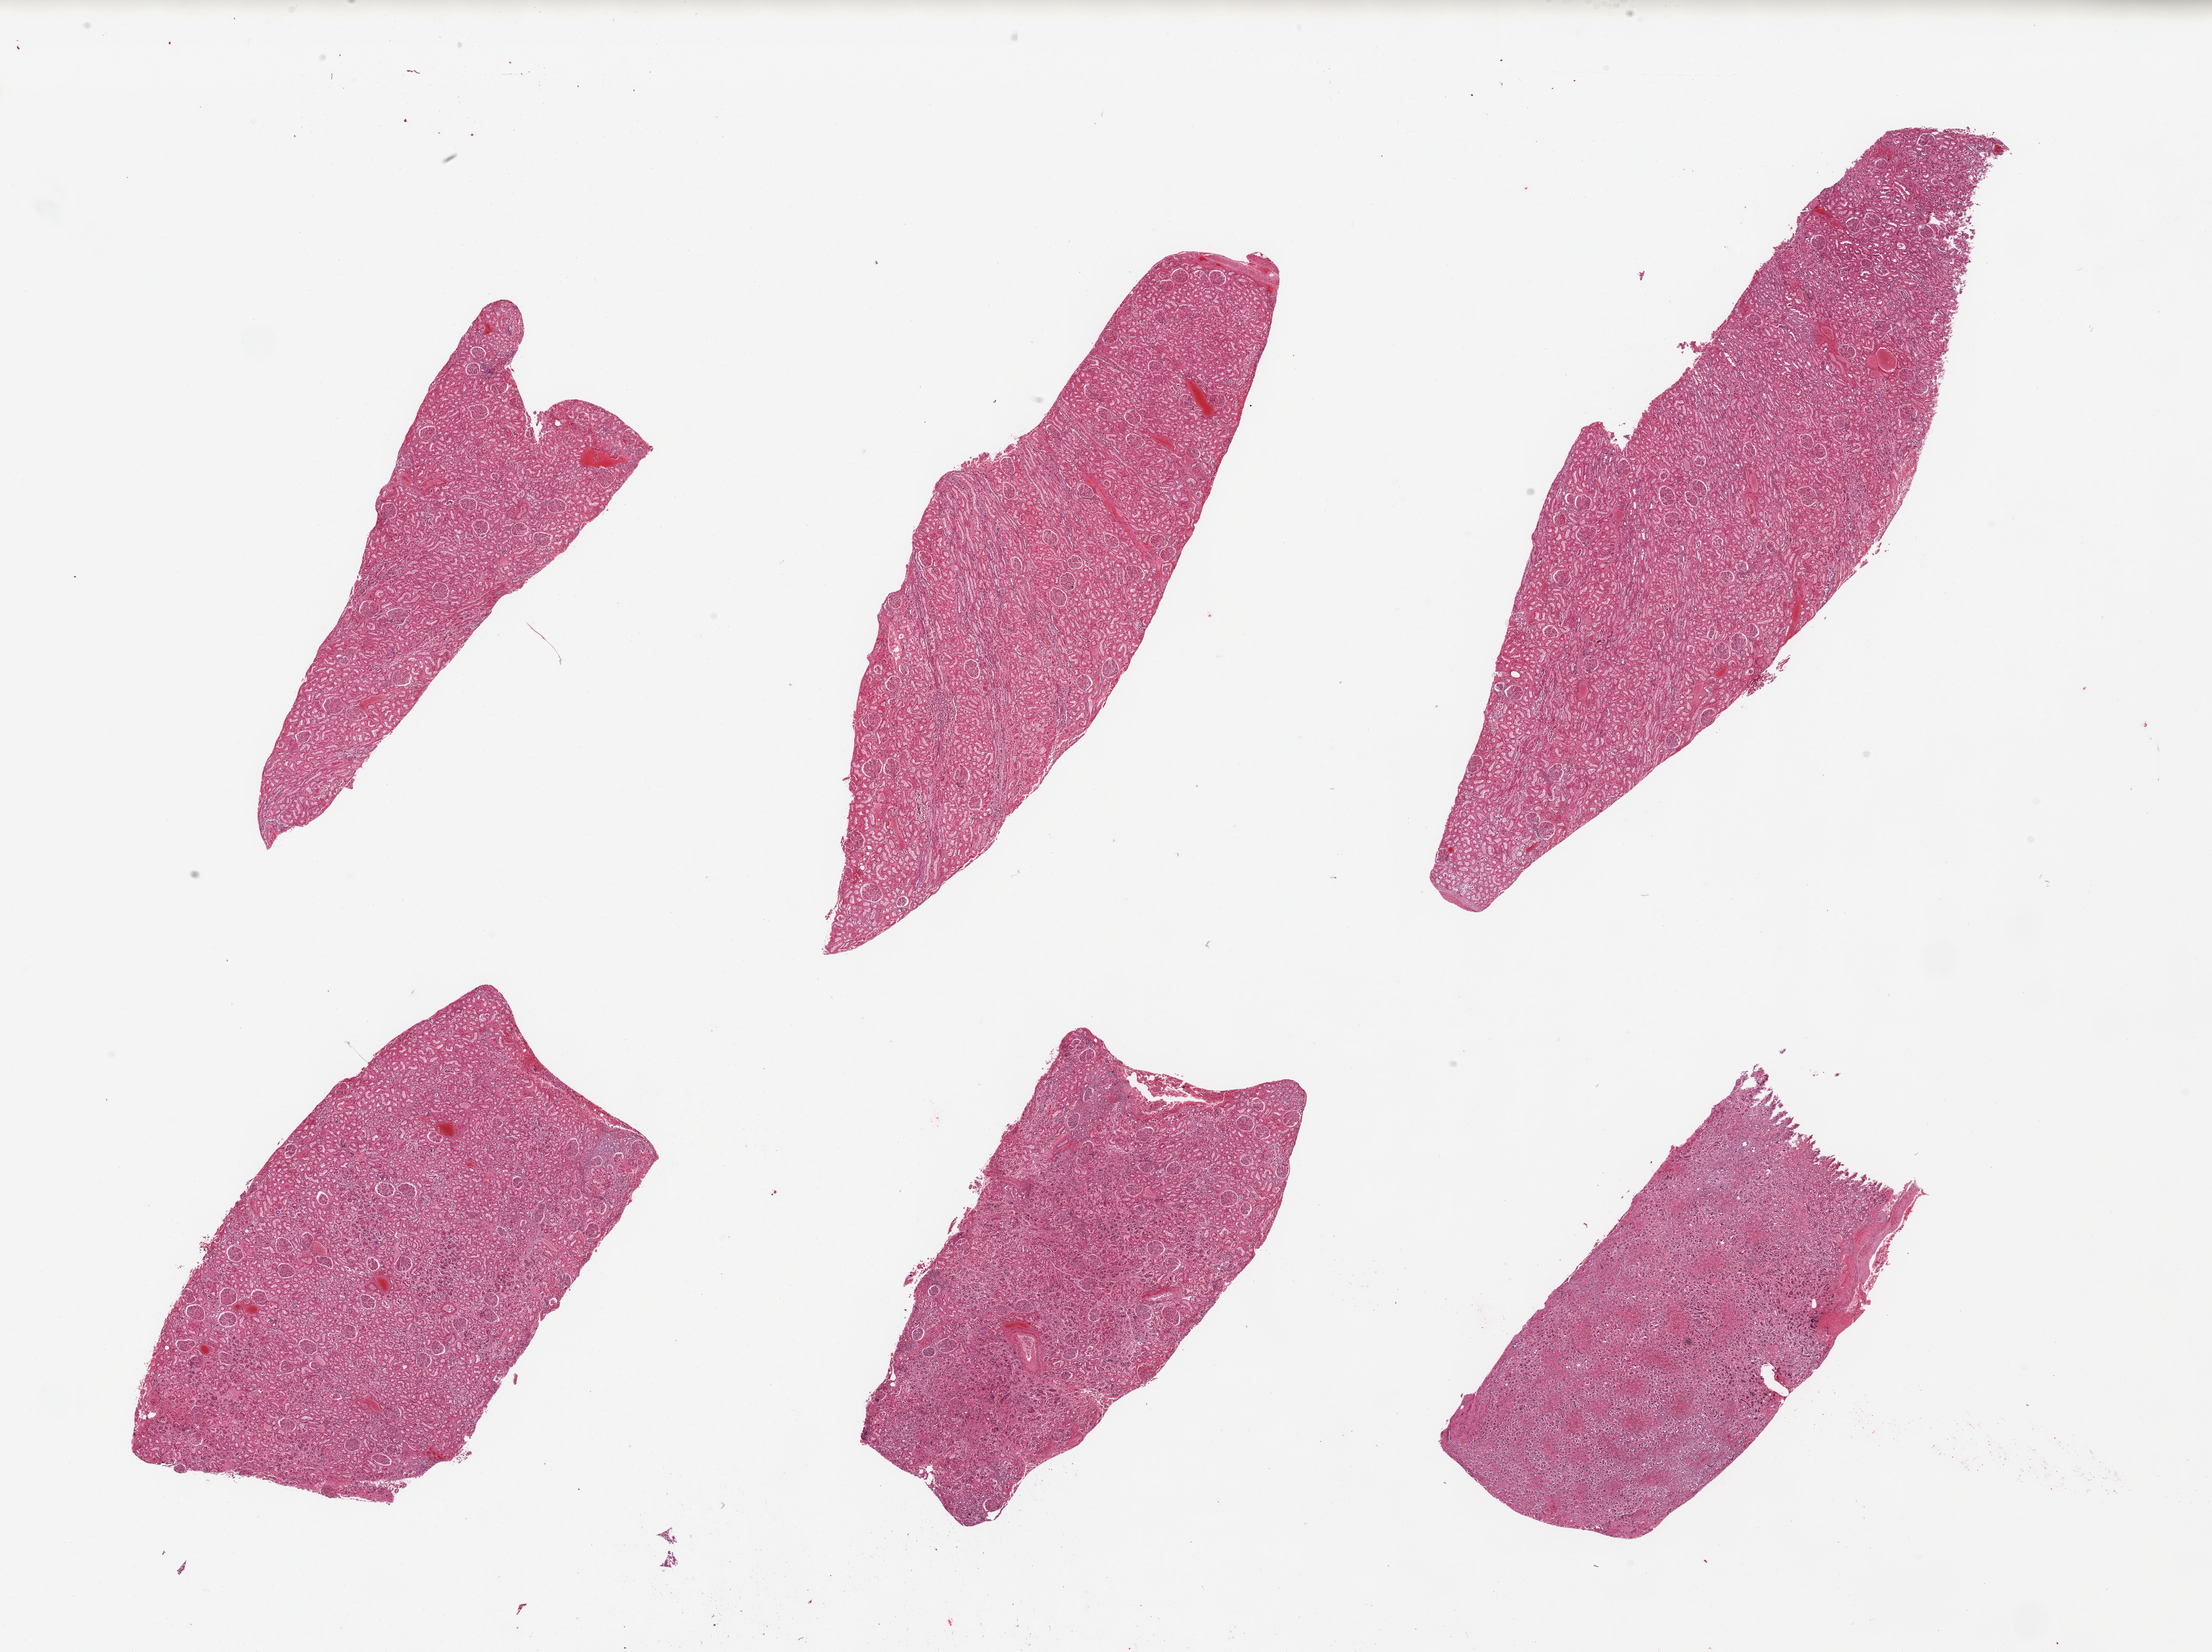
Haematoxylin and eosin whole-slide image, low-resolution overview of the scanned area, about 28.5 x 21.3 mm (from a 20x scan); PAXgene-fixed, paraffin-embedded tissue; target tissue: renal cortex; donor tissue sample.
* pathologist's review note for this sample: 6 pieces: 5 are cortex, 1 is medulla; no sign of active or chronic lesions; glomeruli well preserved, tubules moderately to severely autolyzed